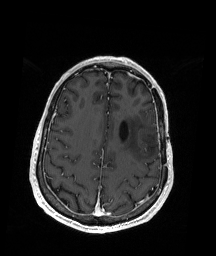
Brain MRI from a brain-tumour surgery series, one axial slice; slice 60 of 192 in the series (ordered by position); T1-weighted post-contrast; 1 mm slice thickness; 216 × 256 image matrix, field of view 211 × 250 mm. Case-level facts recorded for this patient, not image findings: histopathology: Oligodendroglioma; WHO grade: 2; IDH mutation: yes.
Structures marked on this image (manually delineated by an expert):
- previous resection cavity: bounding box [x1, y1, x2, y2] px = [147, 127, 161, 137]